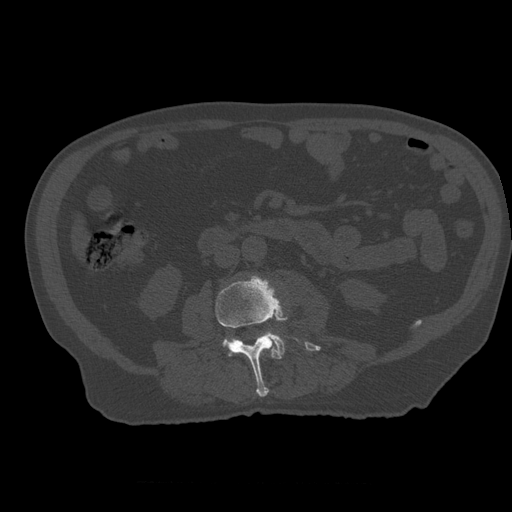
CT including the spine, one axial slice. Slice 186 of 399 in the series (ordered by position). Reconstruction kernel STANDARD. 120 kVp. Bone window (W 1800 / L 400 HU). 1.25 mm slice thickness. 512 × 512 image matrix. Patient age 73 years. From the clinical record (not read from this slice): primary cancer: prostate.
Structures marked on this image (semi-automatically segmented with operator editing):
- L2 vertebra: box from (x=237, y=349) to (x=265, y=356) px
- L3 vertebra: (x=216, y=276)–(x=321, y=397)
- L4 vertebra: (x=225, y=333)–(x=285, y=356)